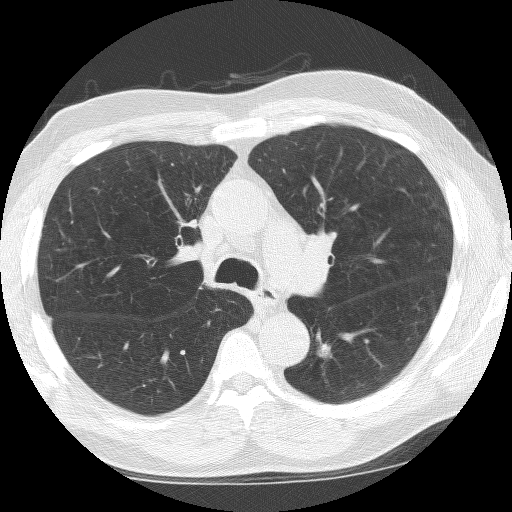
Axial slice from a low-dose chest CT screening exam. First (baseline) screen. Lung window (W 1500 / L -600 HU). 120 kVp. Male, age 67 years at enrolment.
Expert-annotated lung lesion, bounding box (x1, y1, x2, y2) in pixels: (297, 333, 343, 389). Reader record for this screening exam (exam-level; its link to the box is not recorded): non-calcified nodule or mass ≥4 mm, left lower lobe, 18 × 13 mm, spiculated (stellate) margins, soft tissue attenuation. Lung cancer was diagnosed 5 days after this screen: non-small cell carcinoma, left lower lobe, undifferentiated (G4), stage IA (AJCC 6th edition), 12 mm at pathology.